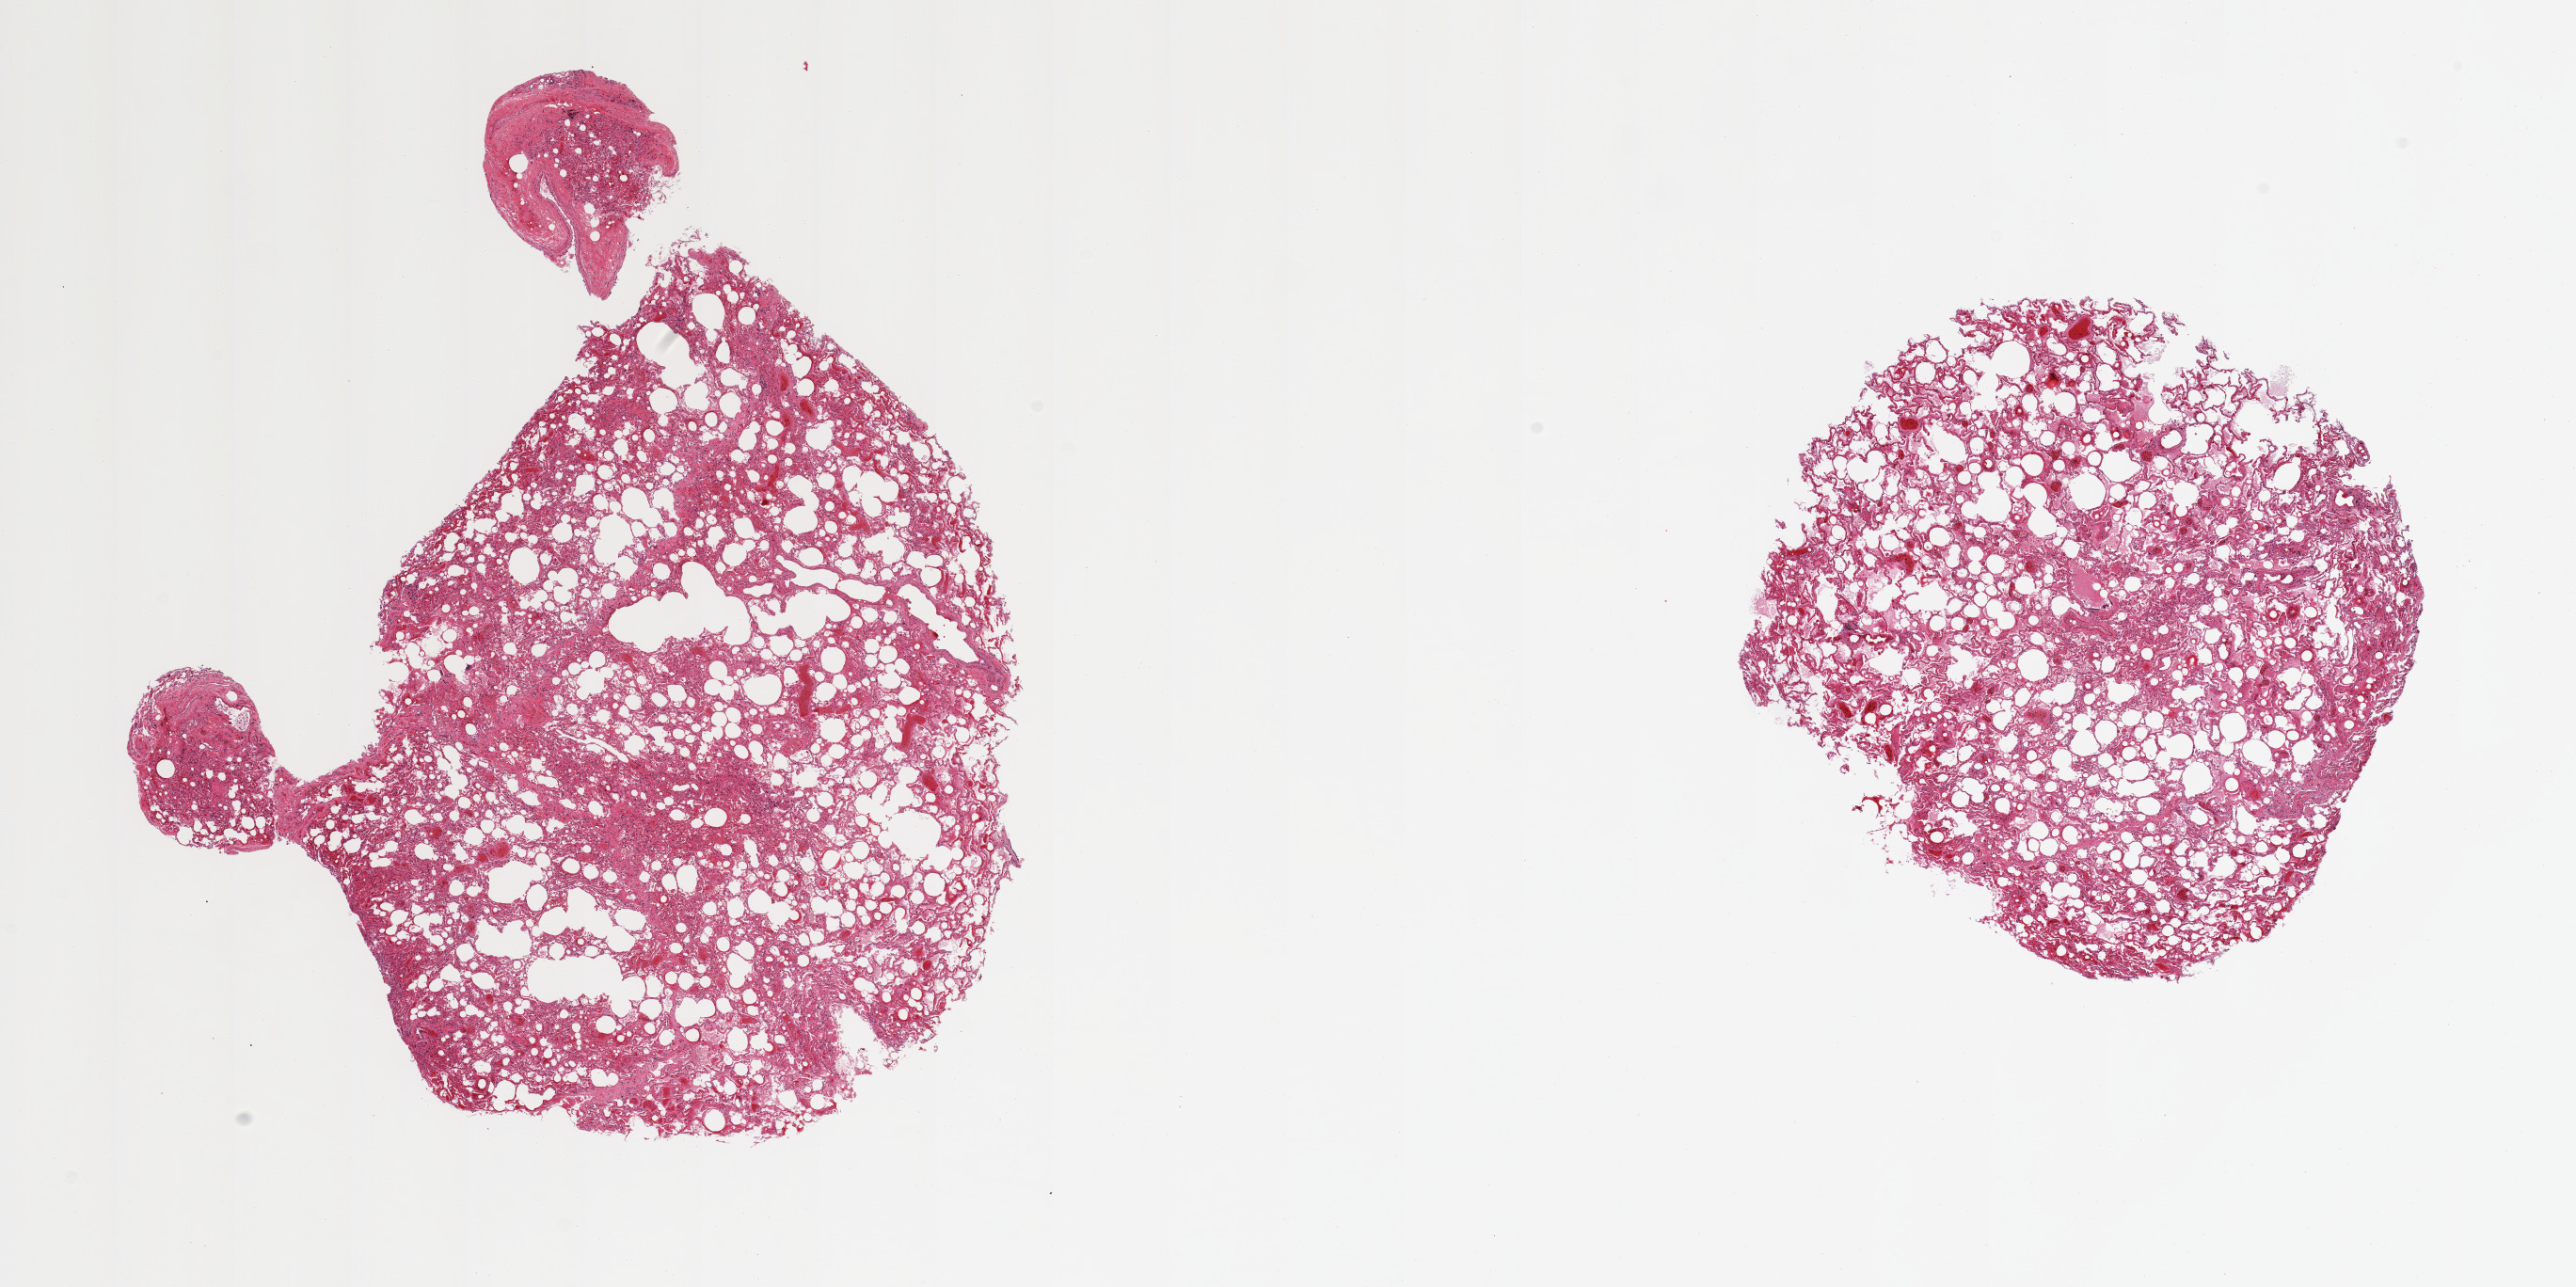
Hematoxylin and eosin (H&E) whole-slide image, brightfield, low-resolution overview of the scanned area, about 21.7 x 10.8 mm, PAXgene-fixed, paraffin-embedded tissue, sampled site (target tissue): lung, donor tissue sample. Donor sex: male.
- reviewer comment on this tissue sample: 2 pieces, patchy moderate congestion